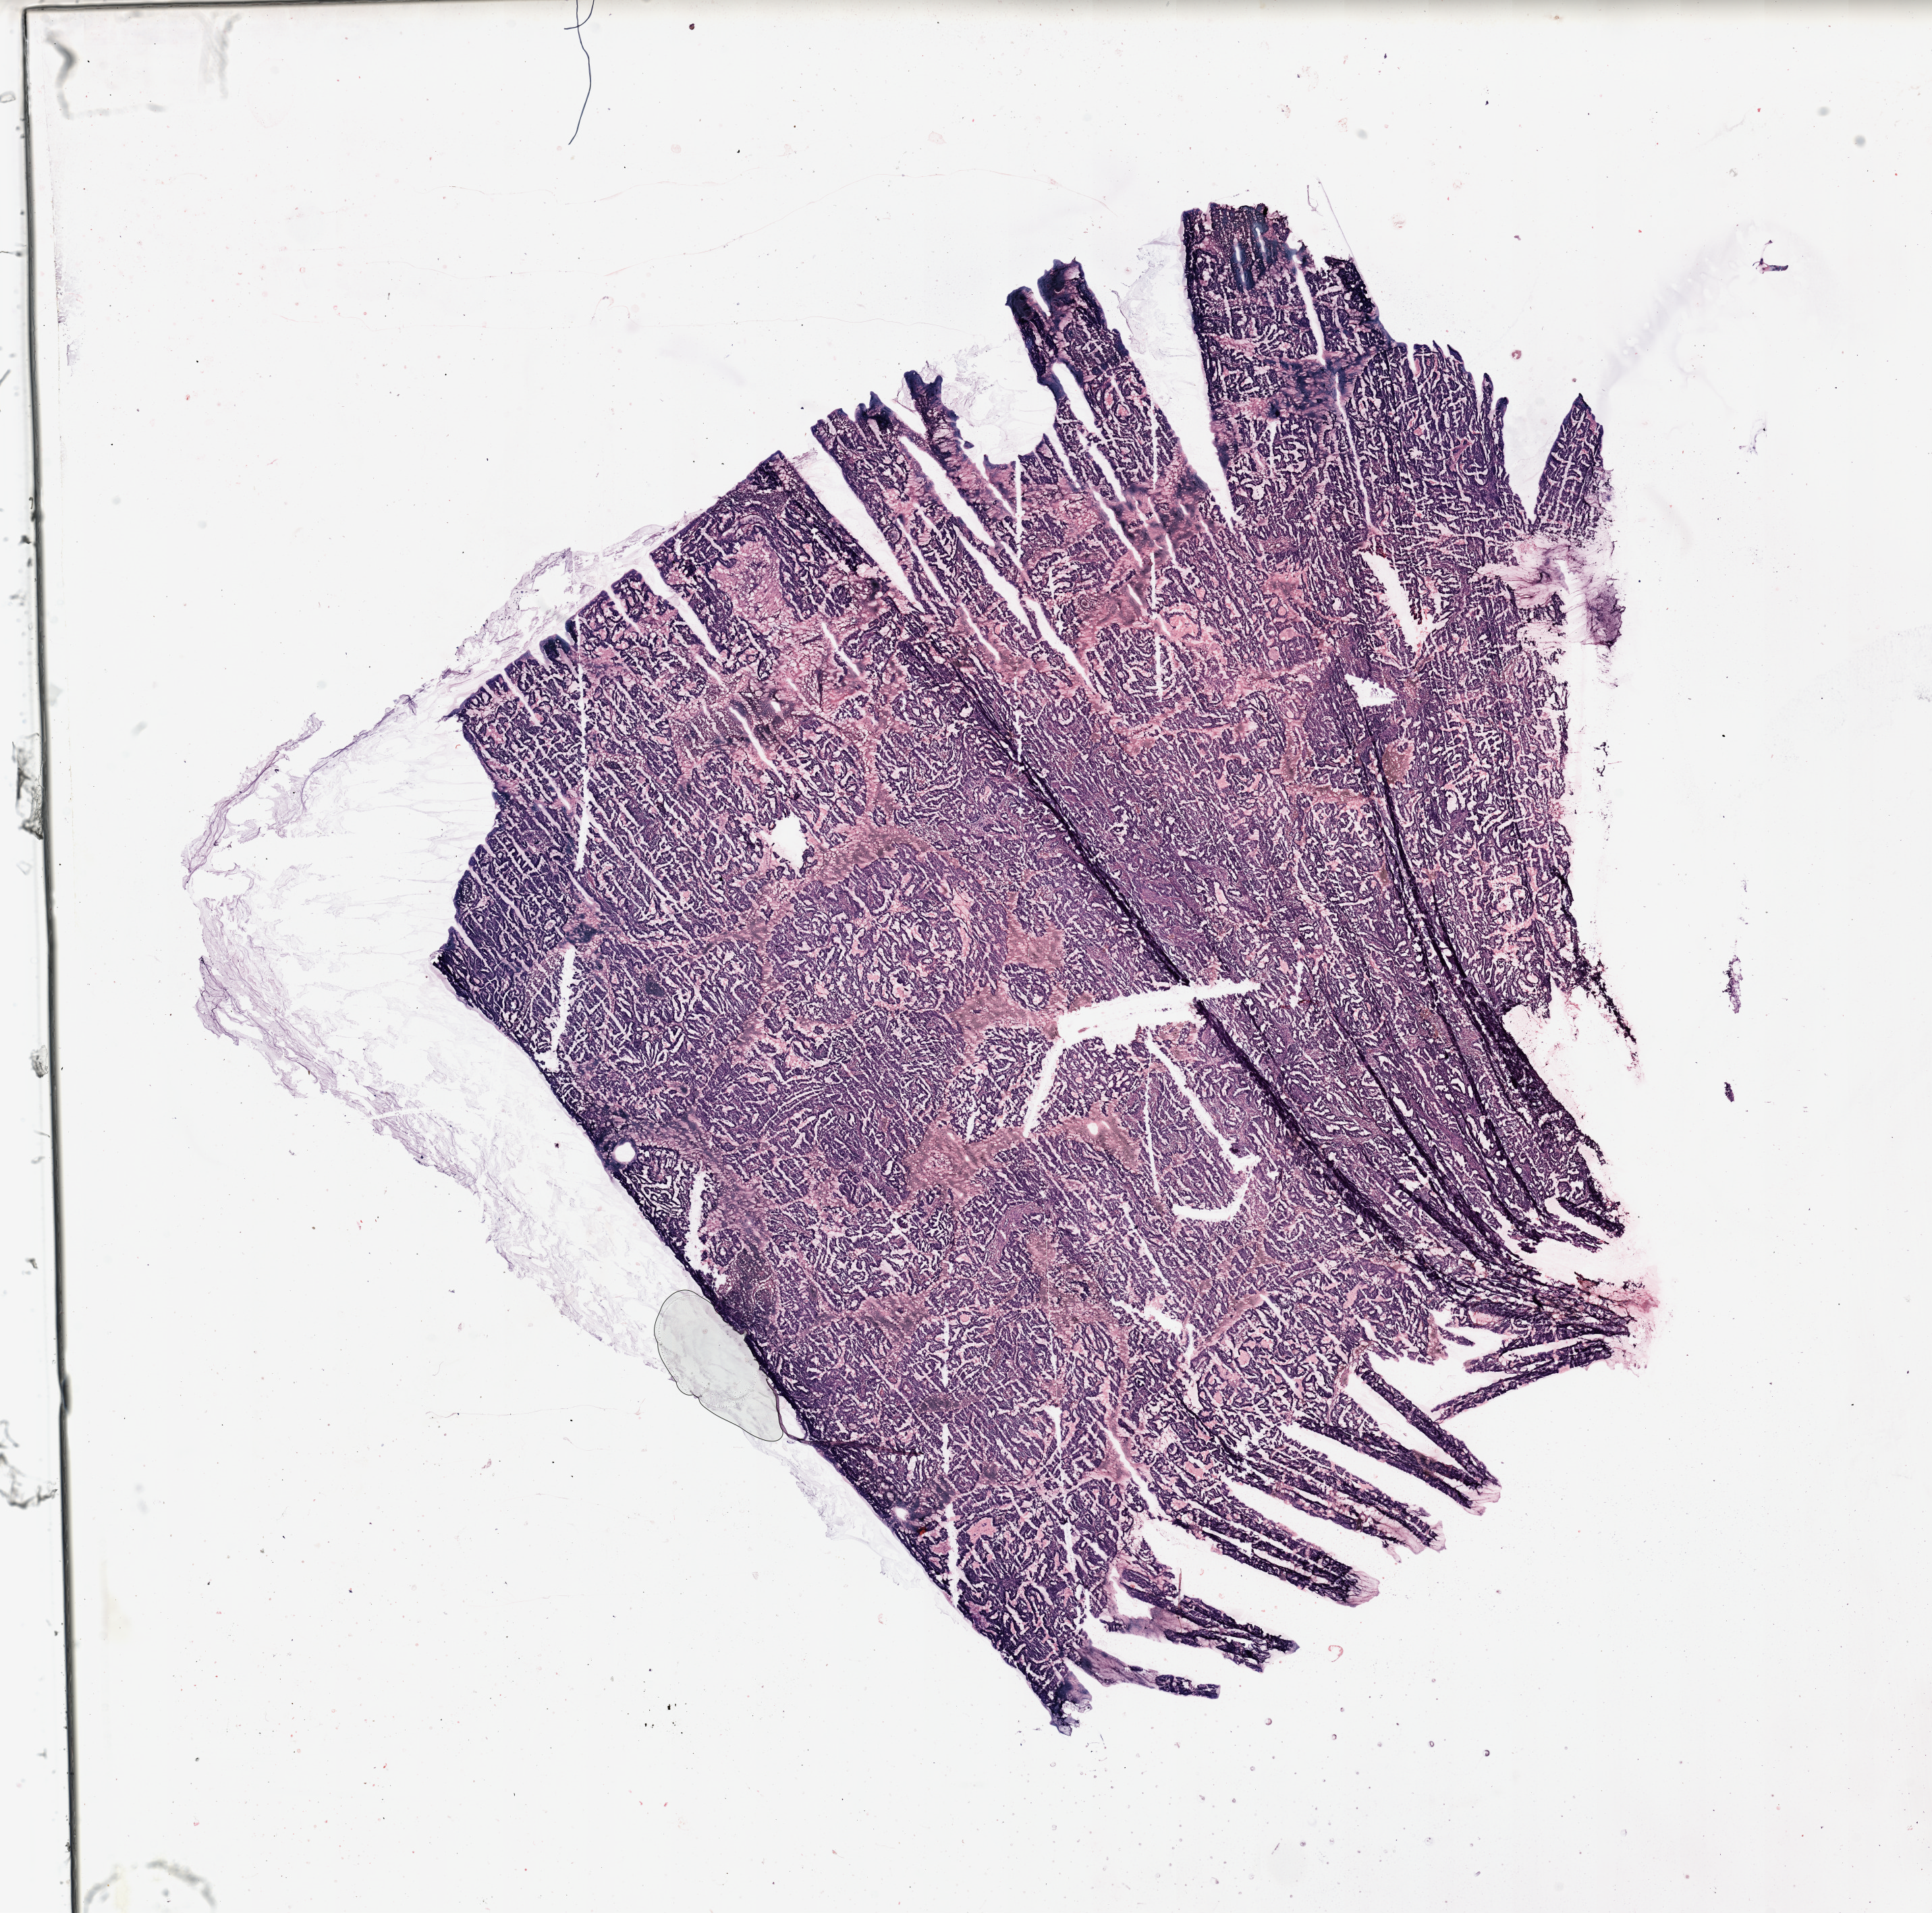
Digitized H&E tissue section (whole slide) — whole scanned area (about 22.6 x 22.4 mm, acquisition: 20x scan) shown as a low-resolution overview. Uterus, tumour tissue. Patient: female, age 64 years. Histologic grade: G2 (moderately differentiated).
- histologic diagnosis: Endometrioid adenocarcinoma, NOS
- AJCC pathologic stage: I